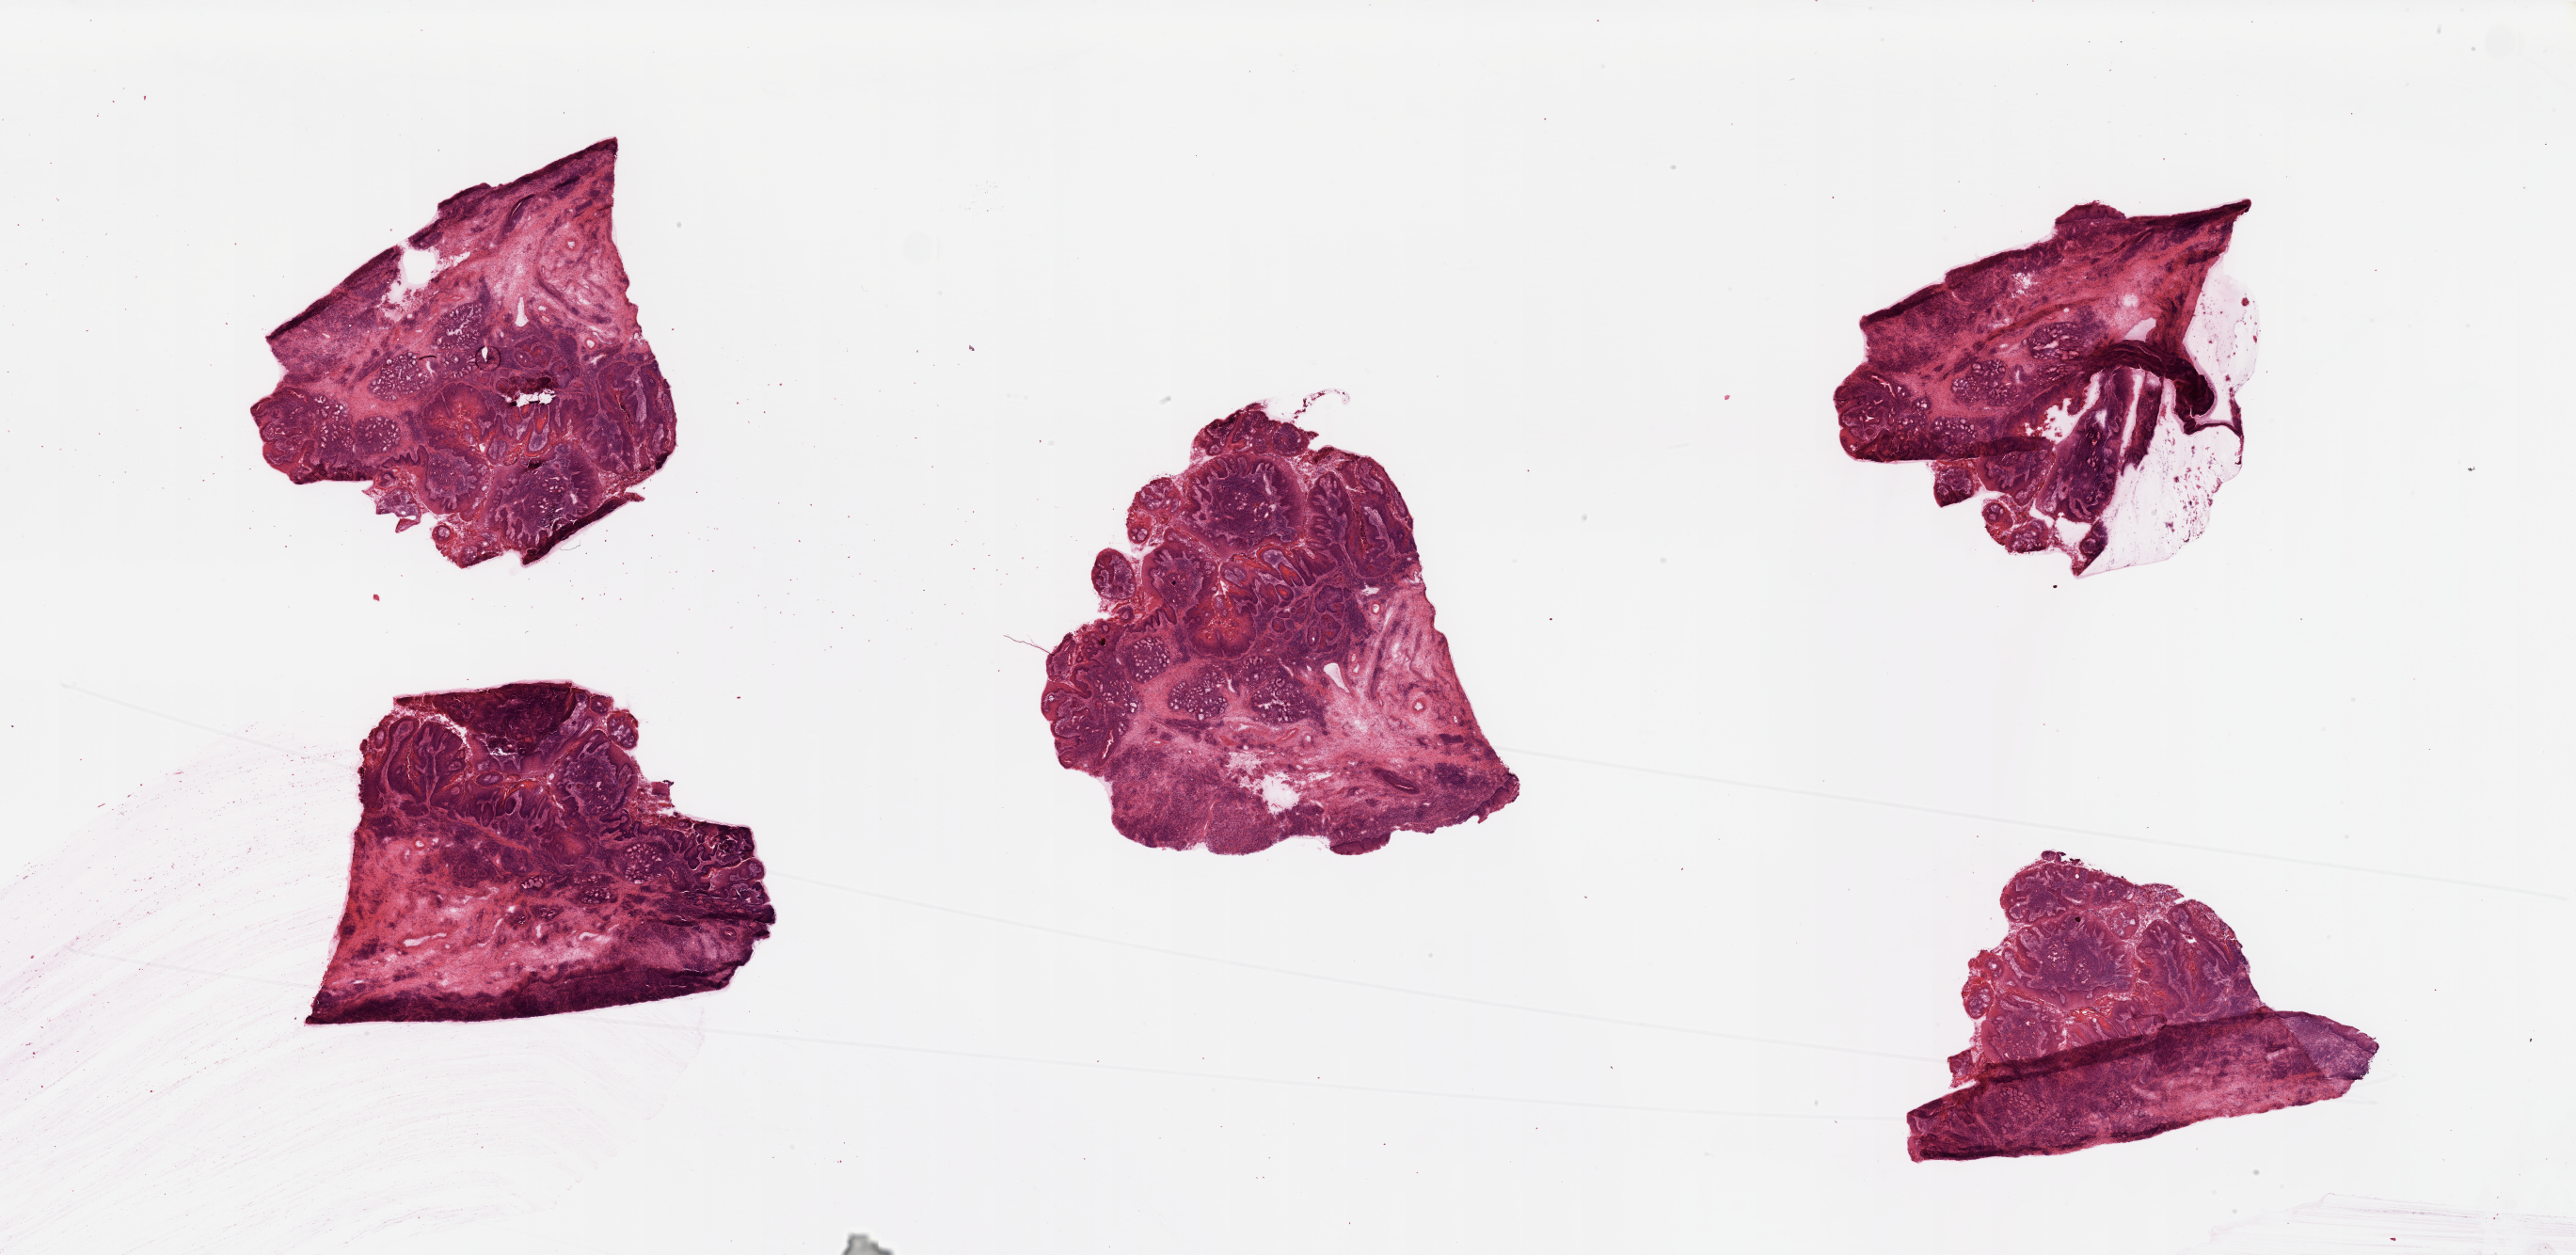
Whole-slide histology image, H&E, shown as a low-resolution overview of the whole scanned area (about 43.3 x 21.1 mm, from a 20x scan), head and neck, tissue type not recorded. 67-year-old male patient.
Patient diagnosis: Squamous cell carcinoma, NOS (larynx, NOS).